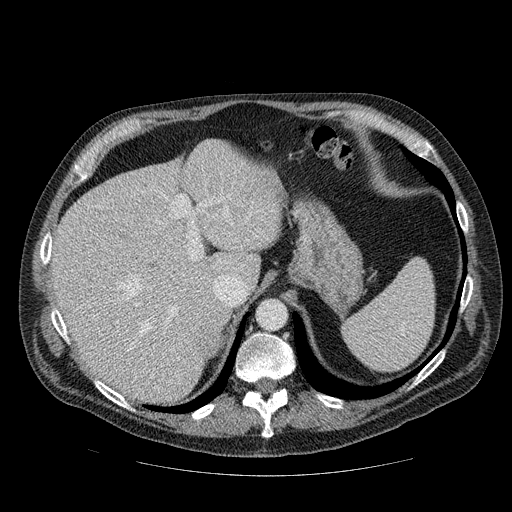
Contrast-enhanced abdominal CT, one axial slice; position 72 of 111 along the scan axis; reconstruction kernel STANDARD; 120 kVp; soft-tissue window (W 400 / L 40 HU); 512 × 512 image matrix, field of view 420 × 420 mm. Patient: male, 56 years. From the clinical record (not read from this slice): diagnosis: adrenocortical carcinoma; tumour side: right adrenal; tumour size at pathology: 9 cm; Ki-67 index: 48 %; stage (as recorded): 4.
Annotated regions visible in this slice (semi-automatically segmented with operator editing):
- mass: bounding box <196,330,219,356> (left, top, right, bottom; pixels)